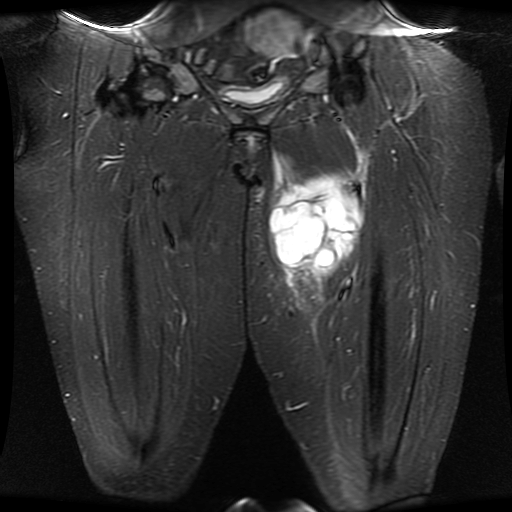
MRI of an extremity soft-tissue mass, one coronal slice. Position 11 of 30 along the scan axis. STIR. 512 × 512 image matrix, field of view 460 × 460 mm. Female patient. From the clinical record (not read from this slice): histological type: myxofibrosarcoma; grade: intermediate; site of the primary tumour: left thigh.
Structures marked on this image (manually delineated by an expert):
- gross tumour volume including surrounding oedema: bounding box <269,150,368,313> (left, top, right, bottom; pixels)
- gross tumour volume (mass): <269,175,361,274>